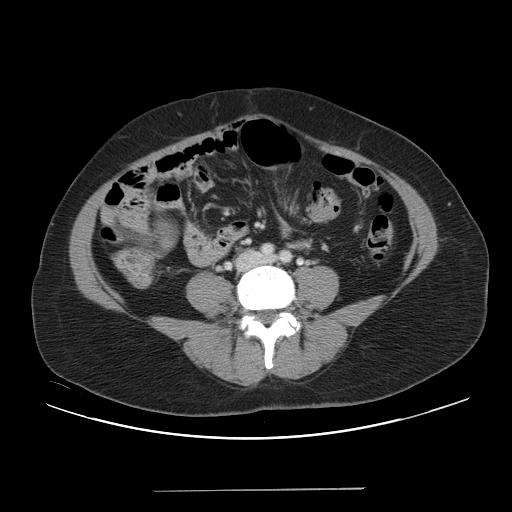
Contrast-enhanced abdominal CT, one axial slice; position 2 of 56 along the scan axis; intravenous contrast given; soft-tissue window (W 400 / L 40 HU); 512 × 512 image matrix, field of view 419 × 419 mm. Female patient, age 54 years. From the clinical record (not read from this slice): diagnosis: colorectal cancer liver metastases, imaged before liver resection; multiple liver metastases: yes; largest metastasis: 3.2 cm; chemotherapy before resection: yes.
Annotated regions visible in this slice (expert manual segmentation):
- liver: box from (x=102, y=209) to (x=113, y=226) px